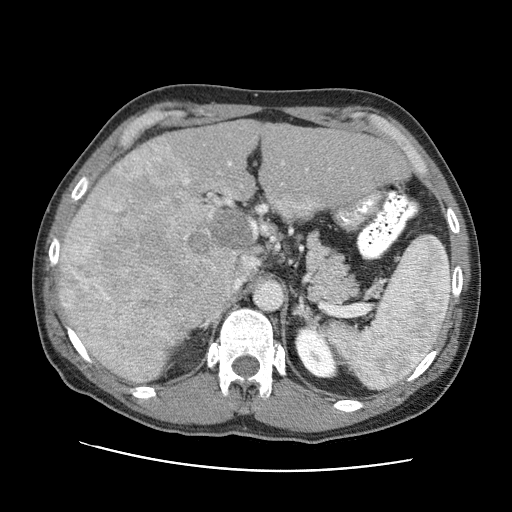
Contrast-enhanced abdominal CT (liver protocol), one axial slice; position 52 of 95 along the scan axis; reconstruction kernel STANDARD; 120 kVp; one of 2 acquisitions stored at this slice position; soft-tissue window (W 400 / L 40 HU); 512 × 512 image matrix, field of view 360 × 360 mm. Case-level facts recorded for this patient, not image findings: diagnosis: hepatocellular carcinoma (patient treated with transarterial chemoembolisation; whether this scan precedes or follows treatment is not stated here); TNM stage (as recorded): Stage-IVA; Child-Pugh class: A; tumour nodularity: multinodular.
Outlined on this slice (semi-automatically segmented with operator editing):
- abdominal aorta: bounding box [x1, y1, x2, y2] px = [256, 282, 282, 309]
- liver parenchyma outside the tumour (the mass and vessels are separate outlines, so this box may not span the whole liver): [58, 120, 410, 324]
- mass: [59, 144, 254, 387]
- liver vessels: [61, 144, 314, 316]